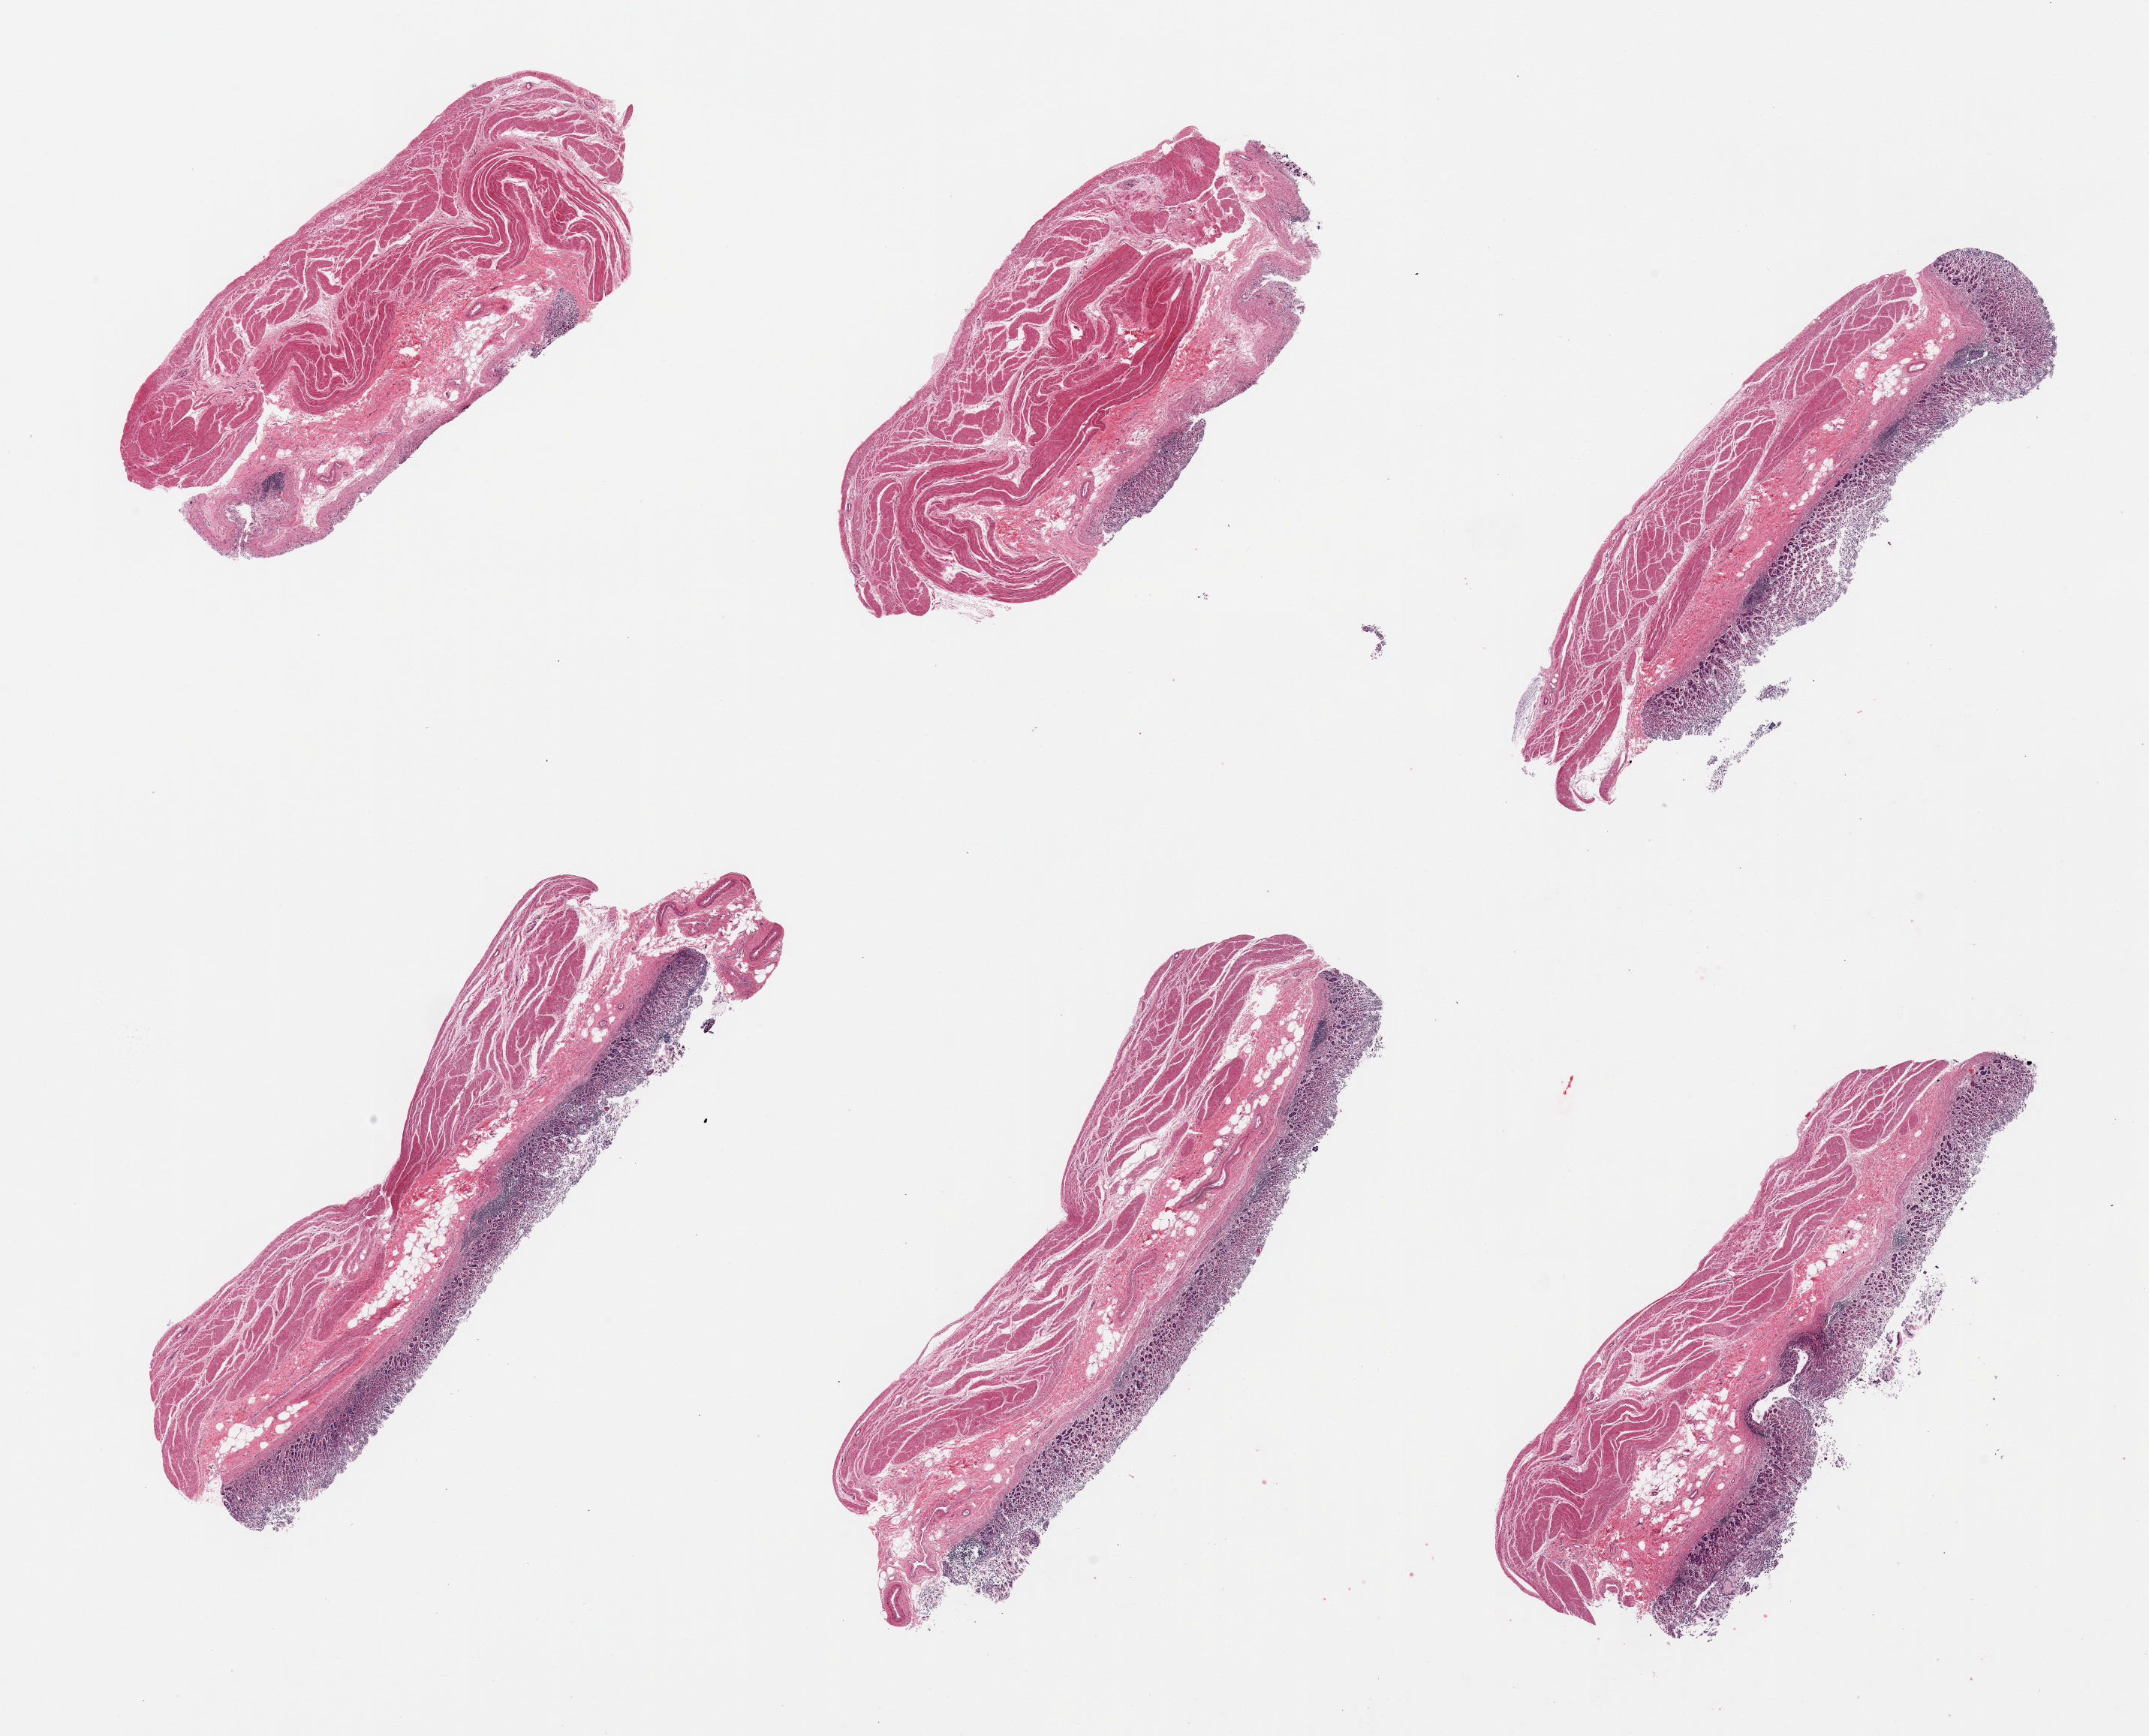
Whole-slide image, haematoxylin and eosin stain — low-resolution overview of the scanned area, about 22.6 x 18.3 mm (acquisition: 20x scan); PAXgene-fixed, paraffin-embedded tissue; section of stomach (target tissue); tissue donor sample. Donor sex: female.
Reviewer comment on this tissue sample: 6 pieces; chronic gastritis; 2 have minimal mucosa.